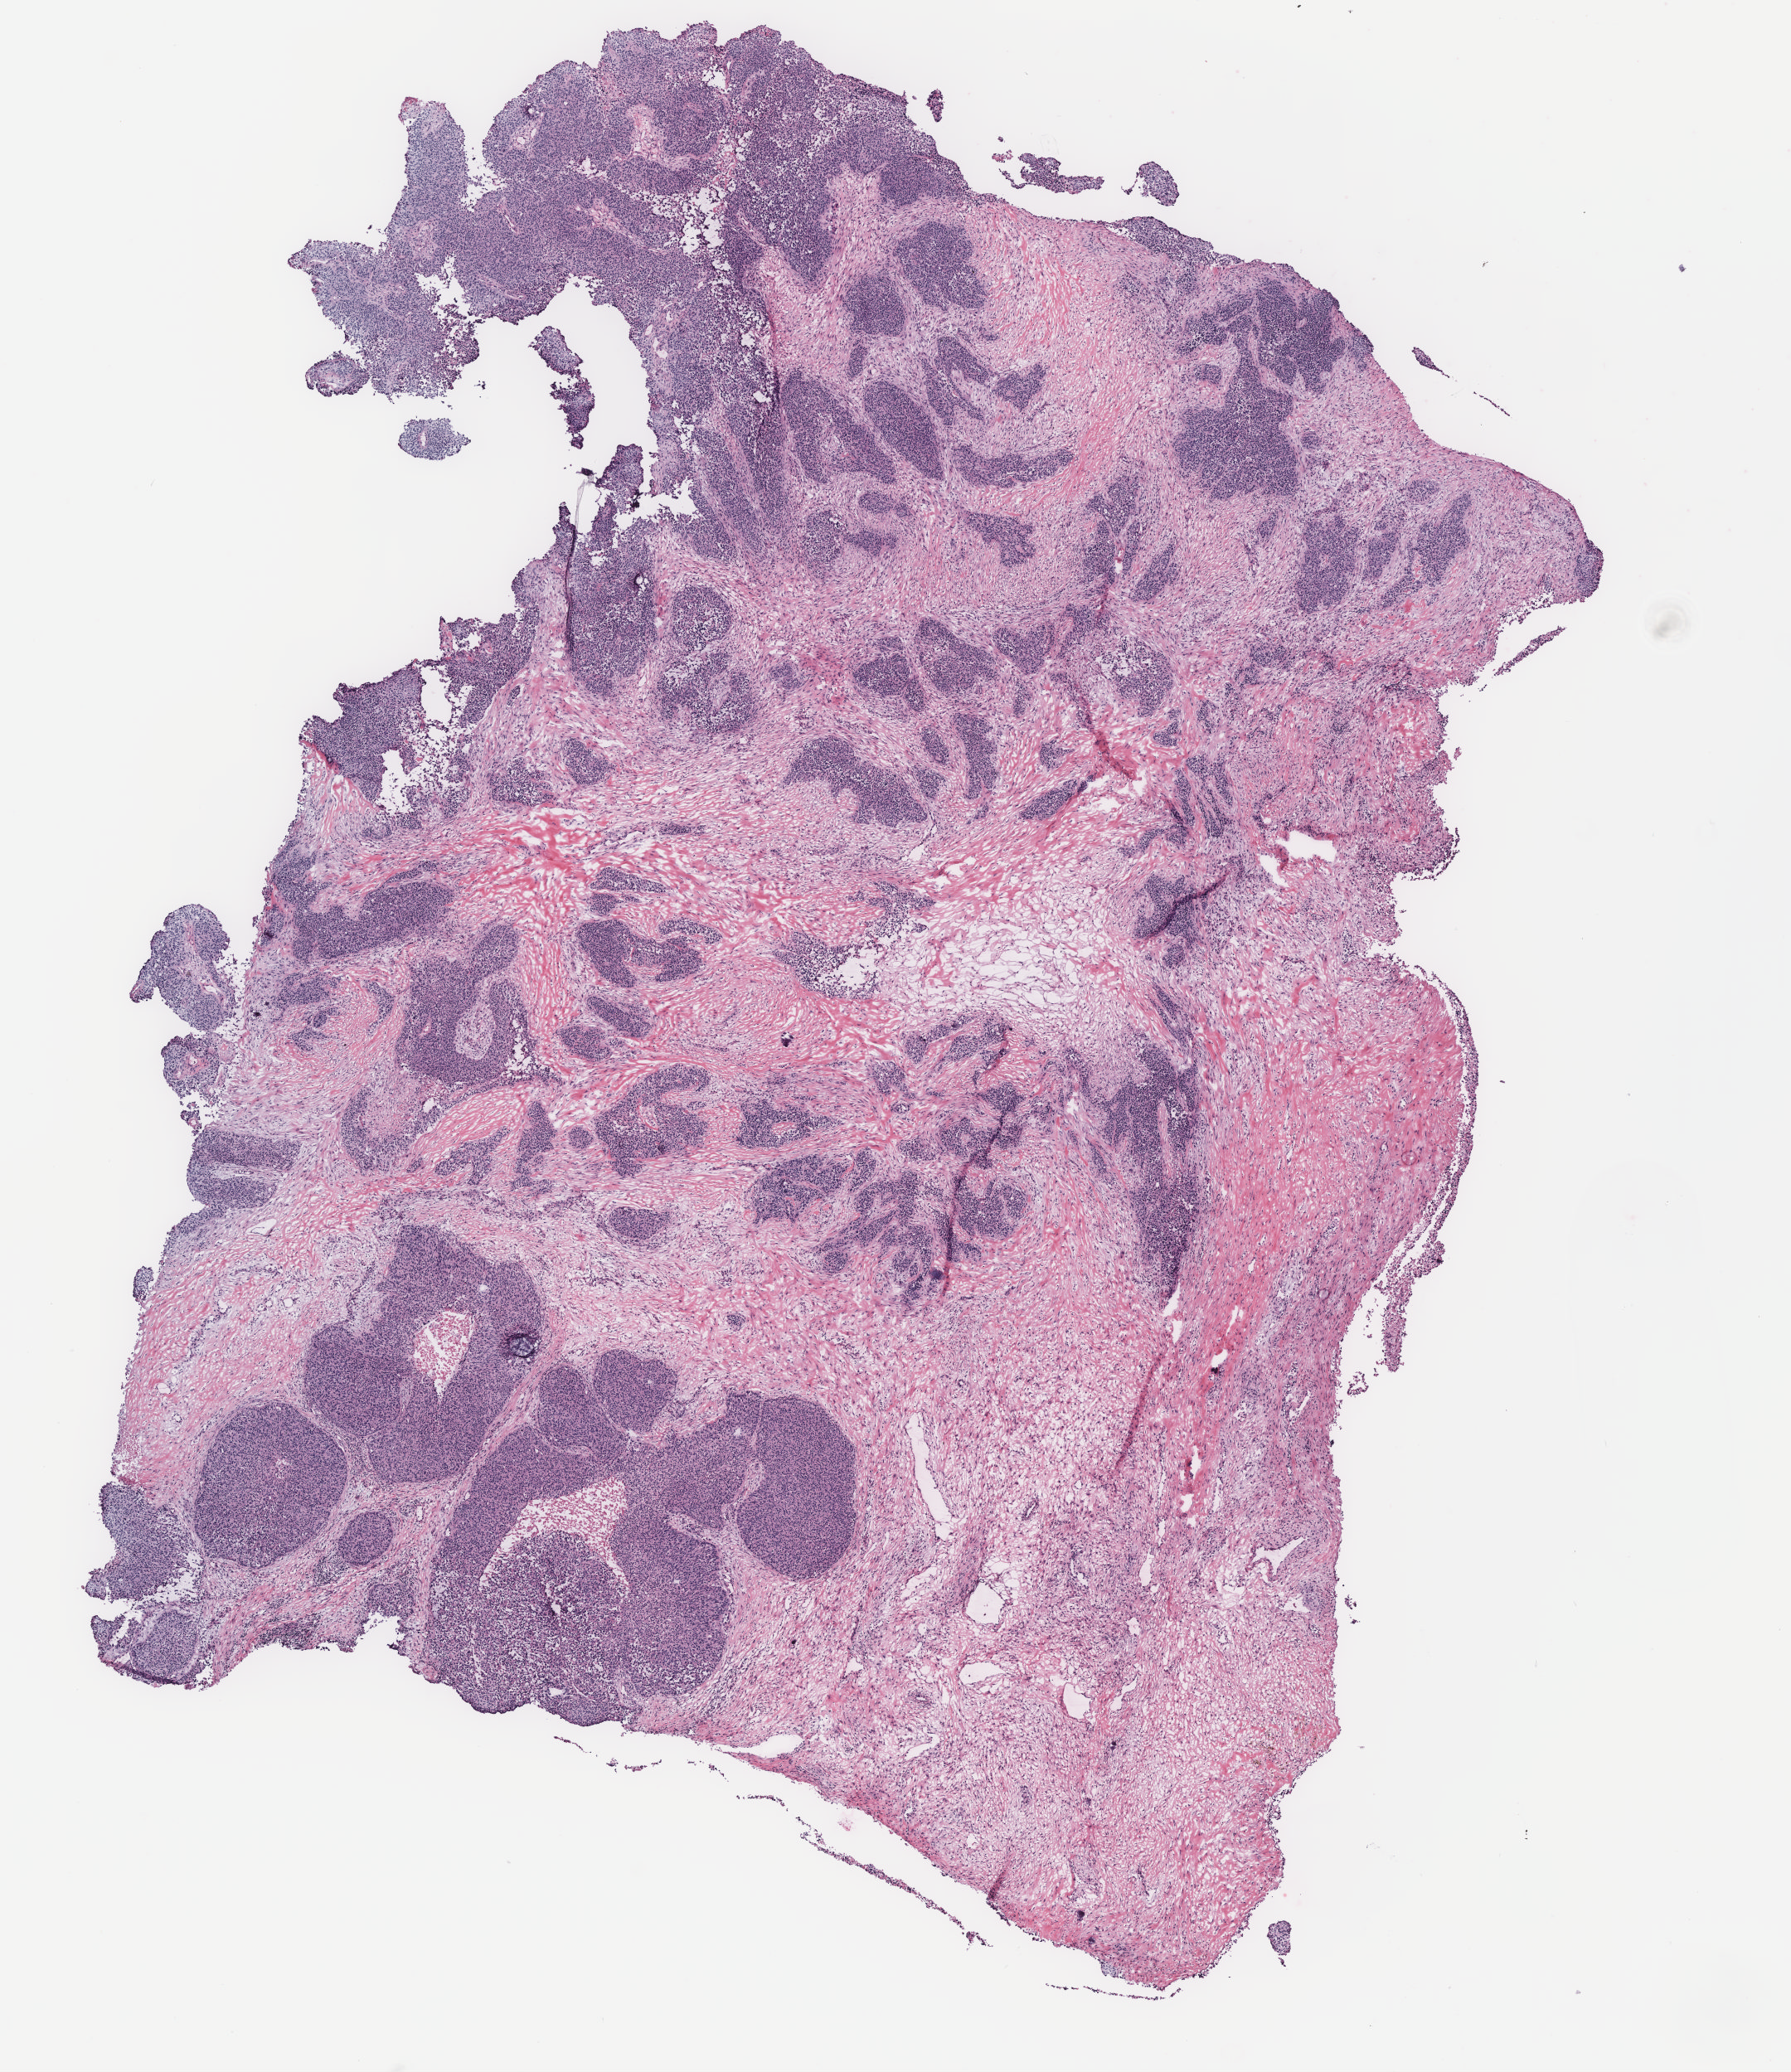
Hematoxylin and eosin (H&E) stained whole-slide image, shown as a low-resolution overview of the whole scanned area (about 8.6 x 10.0 mm), ovary, tissue type not recorded. Female patient.
Patient diagnosis: Serous adenocarcinoma, NOS.